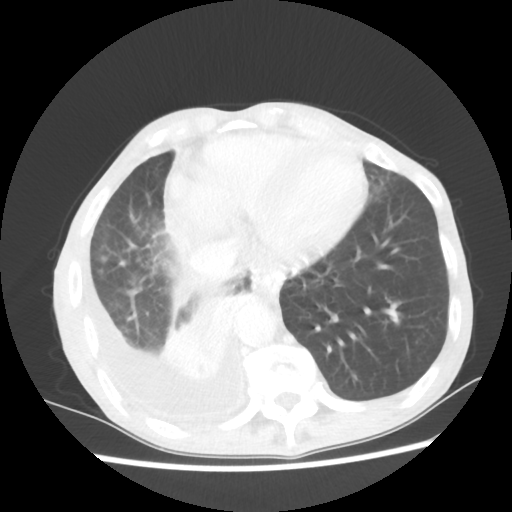
Chest CT, one axial slice. Lung window (W 1500 / L -600 HU). 512 × 512 image matrix, field of view 335 × 335 mm. Patient: male, 76 years. Case-level facts recorded for this patient, not image findings: clinical TNM (as recorded): T3 N3 M1a; histopathological grade: G3.
Structures marked on this image (rectangle marked by the reading radiologist):
- lung tumour (recorded histology: squamous cell carcinoma): box from (x=161, y=289) to (x=253, y=382) px